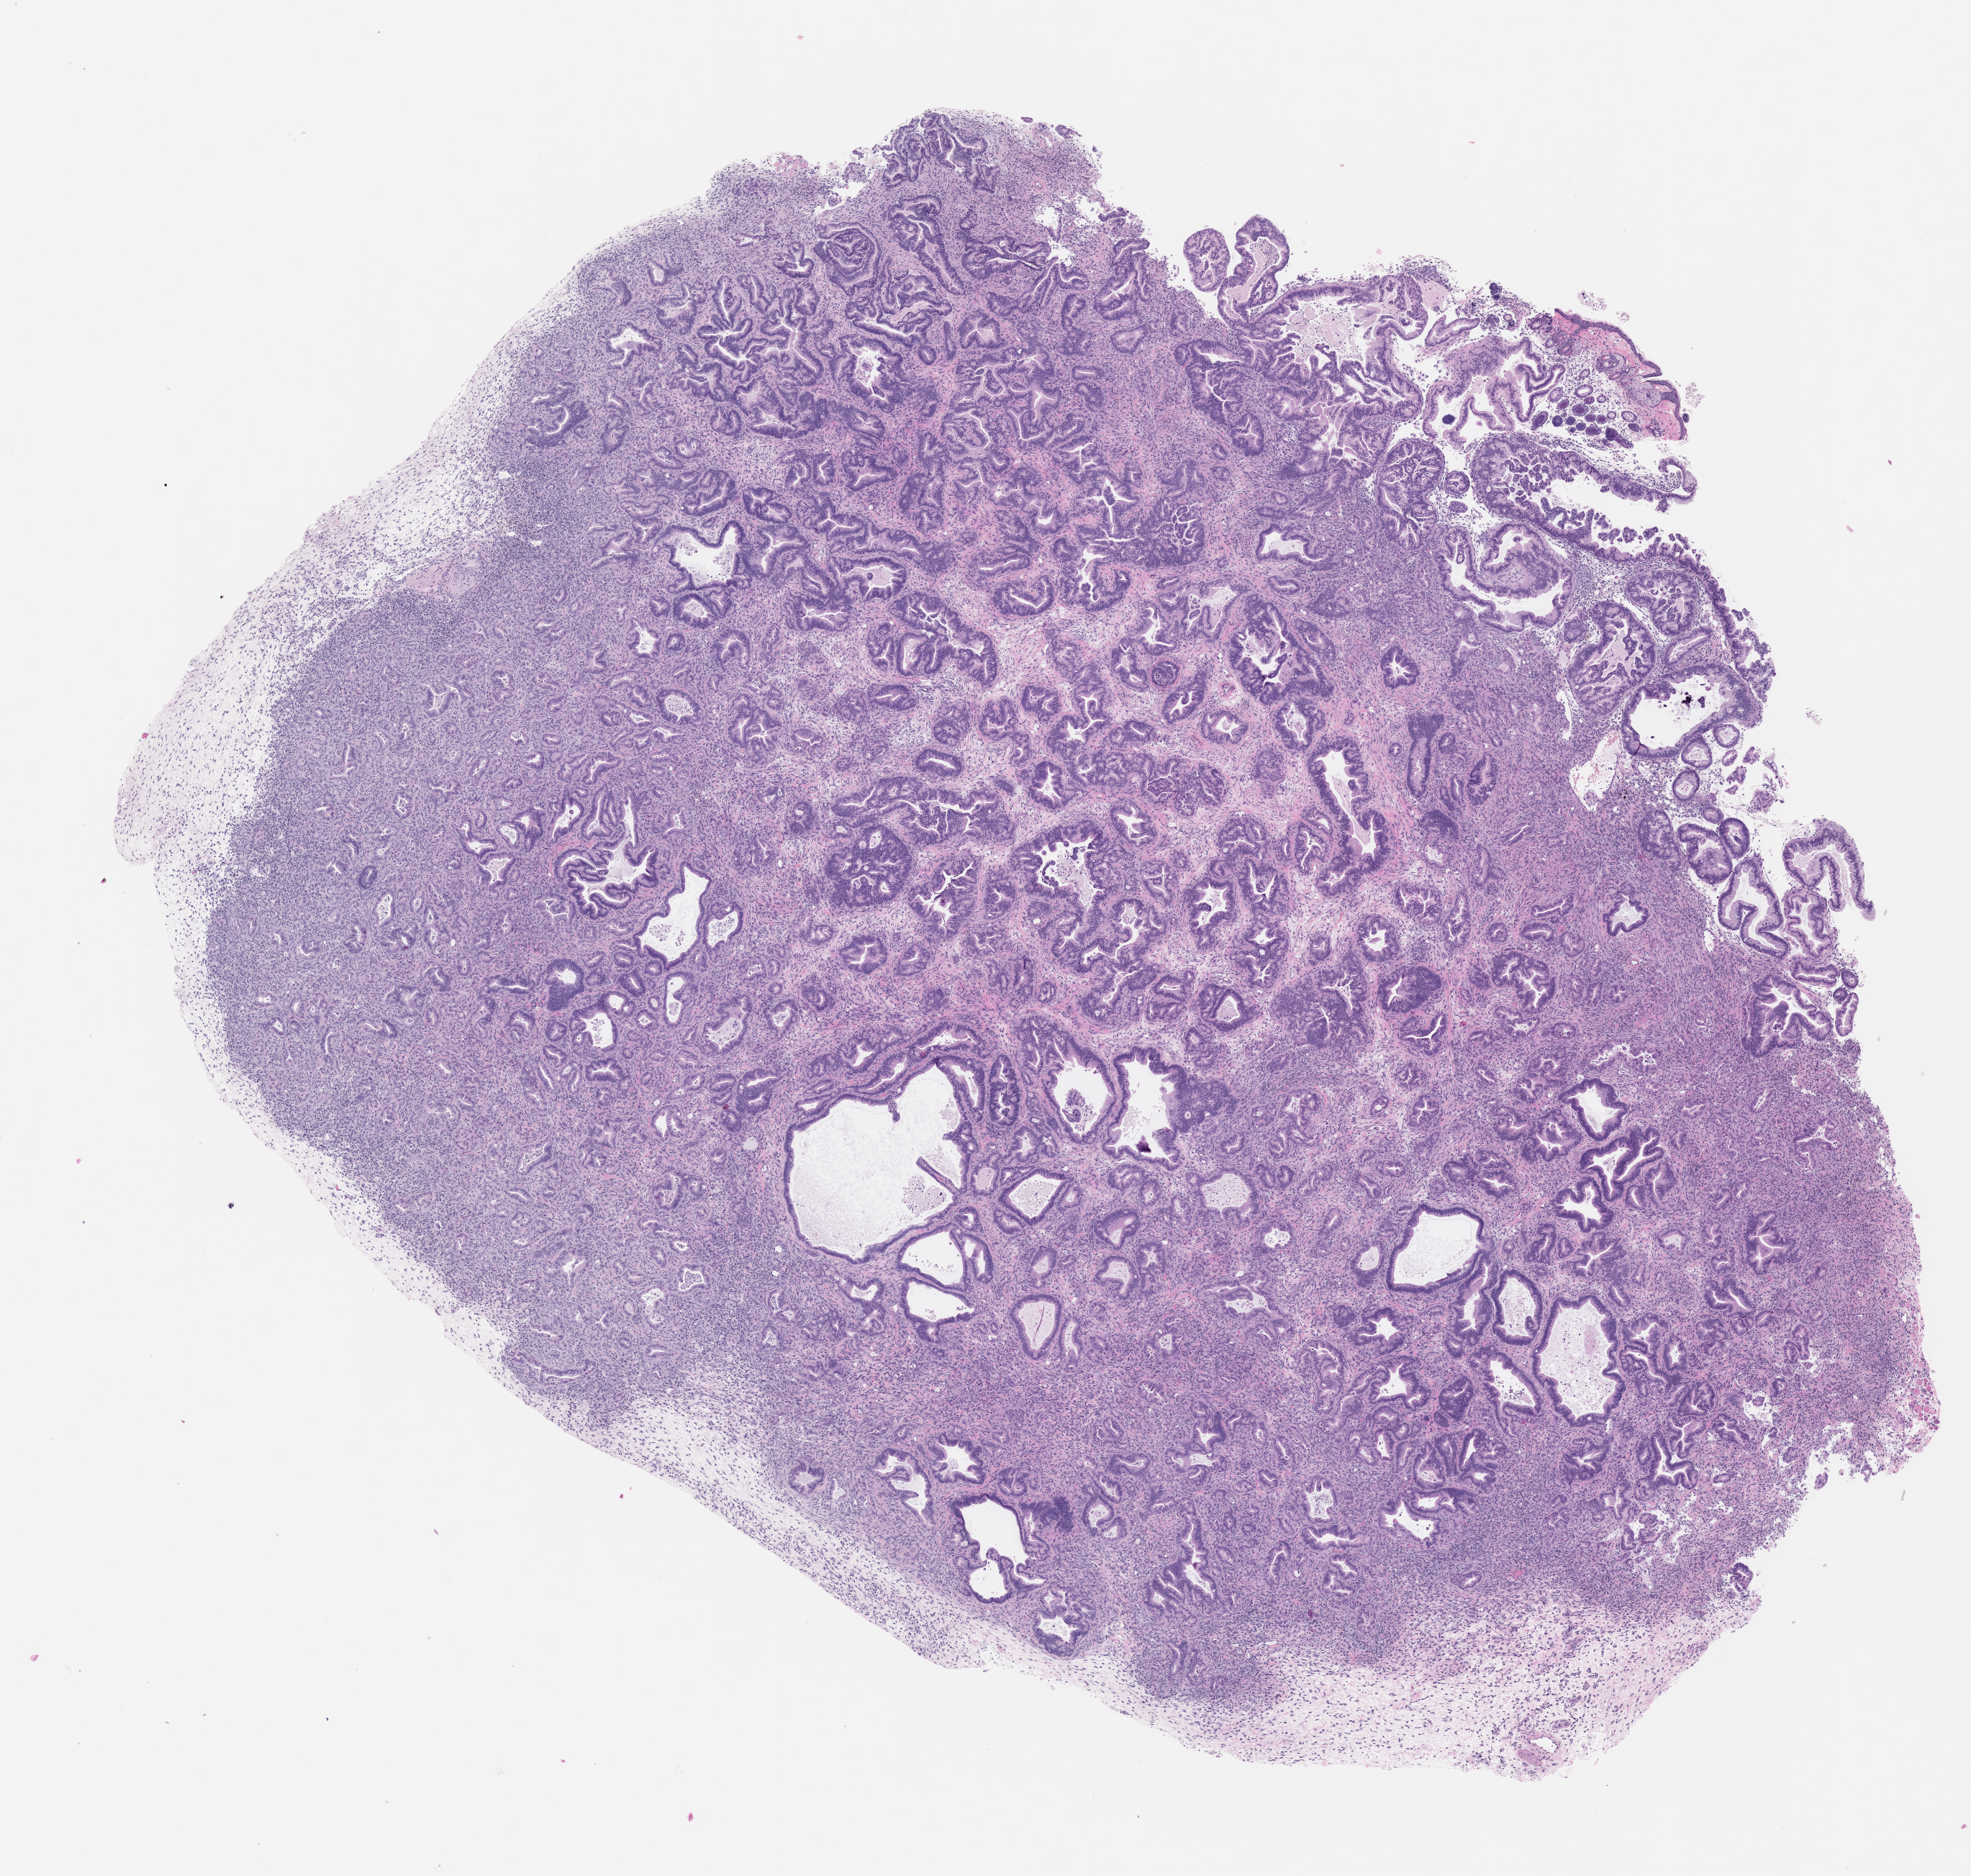
H&E whole-slide image of a patient-derived xenograft (PDX) tumor grown in a mouse, passage 1 — a low-resolution overview of the entire scanned area, about 11.0 x 10.5 mm. Formalin-fixed paraffin-embedded section. Tumor site category: pancreas.
Originating patient diagnosis: Pancreatic Adenocarcinoma.